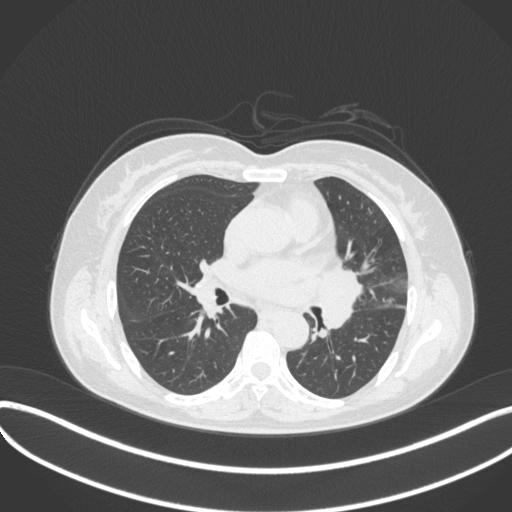
Chest CT, one axial slice. Position 186 of 373 along the scan axis. Lung window (W 1500 / L -600 HU). 1 mm slice thickness. 512 × 512 image matrix, field of view 400 × 400 mm. Female patient, age 54 years. From the clinical record (not read from this slice): clinical TNM (as recorded): T2a N1 M0; histopathological grade: G3.
Structures marked on this image (bounding box drawn by a radiologist):
- lung tumour (recorded histology: small cell carcinoma): bounding box [x1, y1, x2, y2] px = [313, 265, 364, 339]